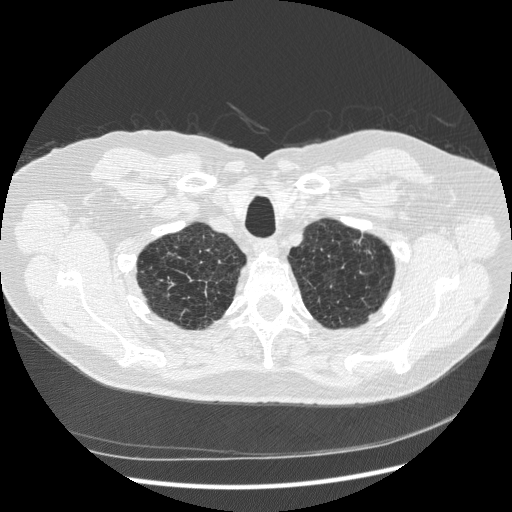
Chest CT (low-dose screening protocol), one axial image; first (baseline) screen; lung window (W 1500 / L -600 HU). Male participant, aged 70 years at enrolment. Former smoker at enrolment.
Lesion marked by an expert reader, bounding box <333,222,390,279> (left, top, right, bottom; pixels). The screening reader recorded 2 non-calcified nodules or masses ≥4 mm on this exam (right lower lobe, right lower lobe); which of them this box marks is not recorded. Participant outcome: lung cancer diagnosed 816 days after this screen (after the third annual screen) — squamous cell carcinoma, NOS, left upper lobe, moderately differentiated (G2), stage IA (AJCC 6th edition), 18 mm at pathology.